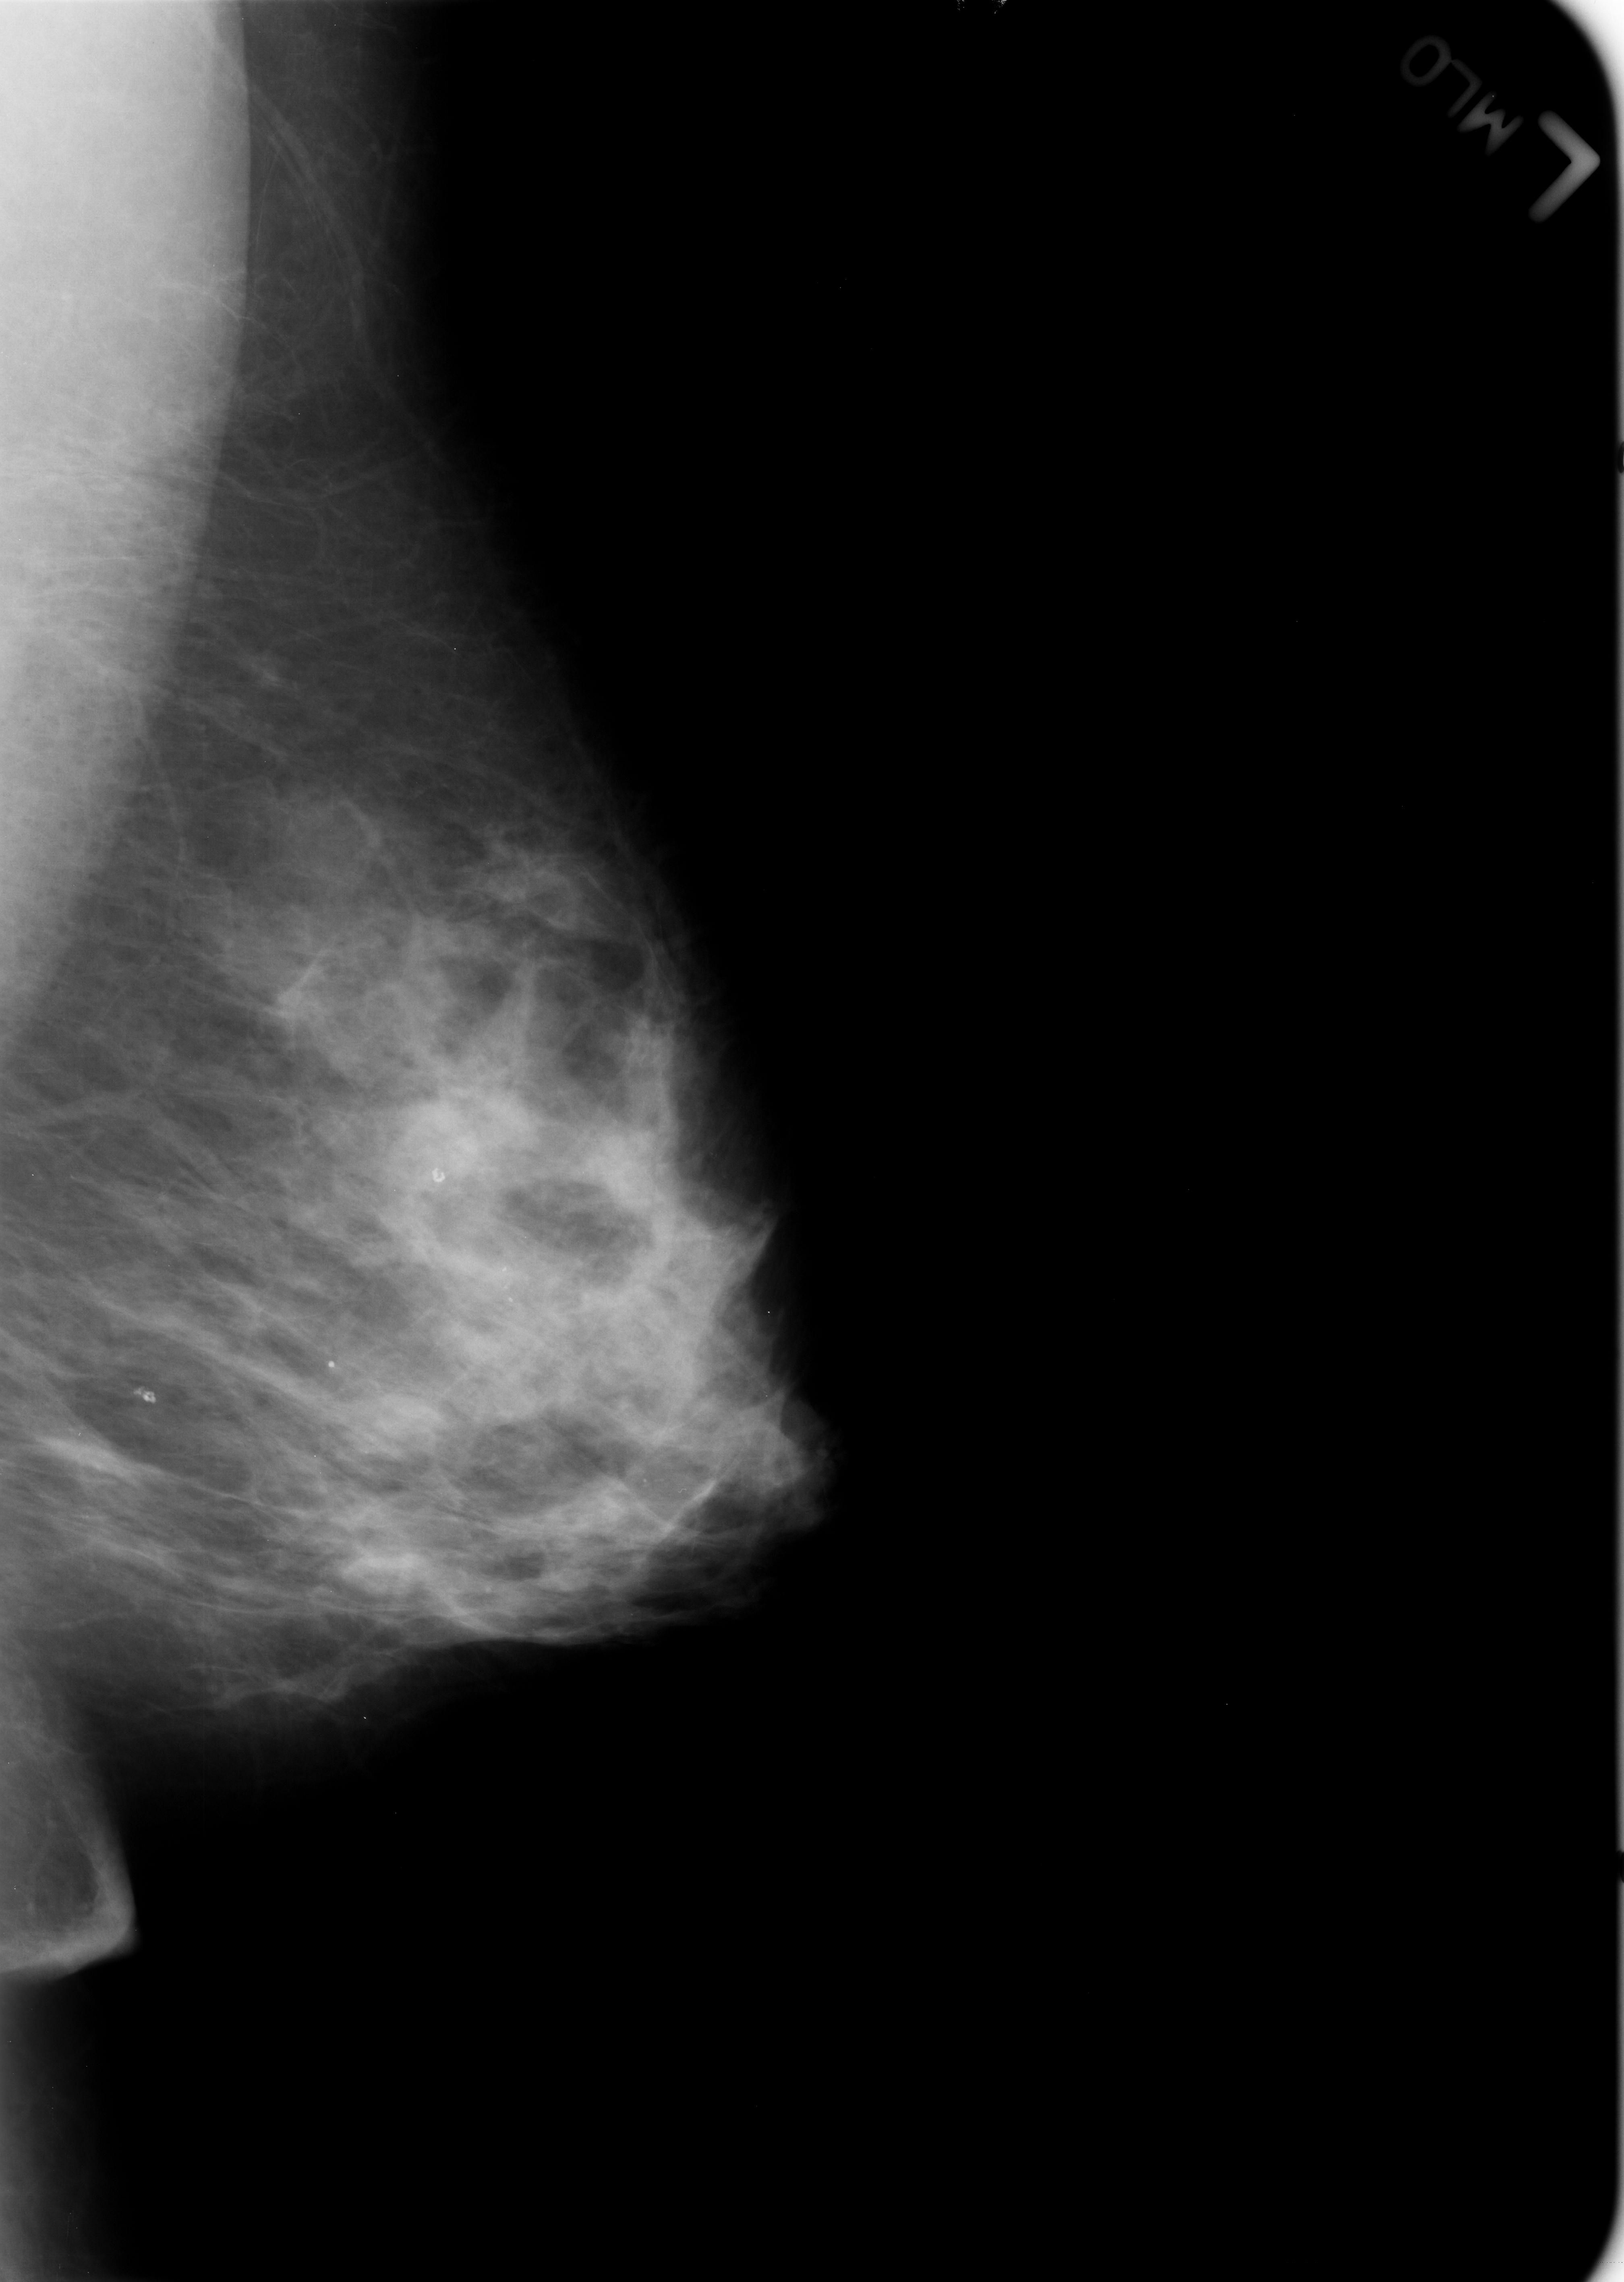
Digitized screen-film mammogram, left breast, MLO view, breast composition: heterogeneously dense (BI-RADS density category 3 of 4).
- Radiologist-marked abnormalities on this image: Finding 1 of 3: calcifications, morphology round and regular / lucent center; BI-RADS assessment category 2; benign; no additional work-up was recommended (benign without callback).
- Finding 2 of 3: calcifications, morphology round and regular / lucent center; BI-RADS assessment category 2; benign without callback (not worked up further).
- Finding 3 of 3: calcifications, morphology round and regular / lucent center; BI-RADS assessment category 2; benign; no additional work-up was recommended (benign without callback).